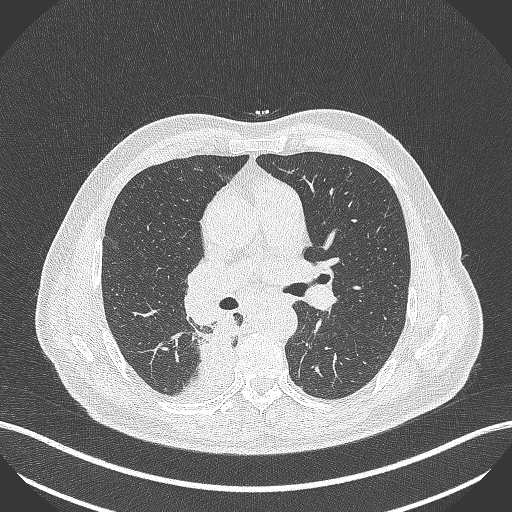
Chest CT, one axial slice; position 268 of 451 along the scan axis; reconstruction kernel B70f; 100 kVp; lung window (W 1500 / L -600 HU); 1 mm slice thickness; 512 × 512 image matrix, field of view 400 × 400 mm. Patient: male, 61 years. Case-level facts recorded for this patient, not image findings: clinical TNM (as recorded): T1 N0 M0; histopathological grade: G3.
Structures marked on this image (rectangle marked by the reading radiologist):
- lung tumour (recorded histology: small cell carcinoma): bounding box [x1, y1, x2, y2] px = [198, 314, 240, 366]